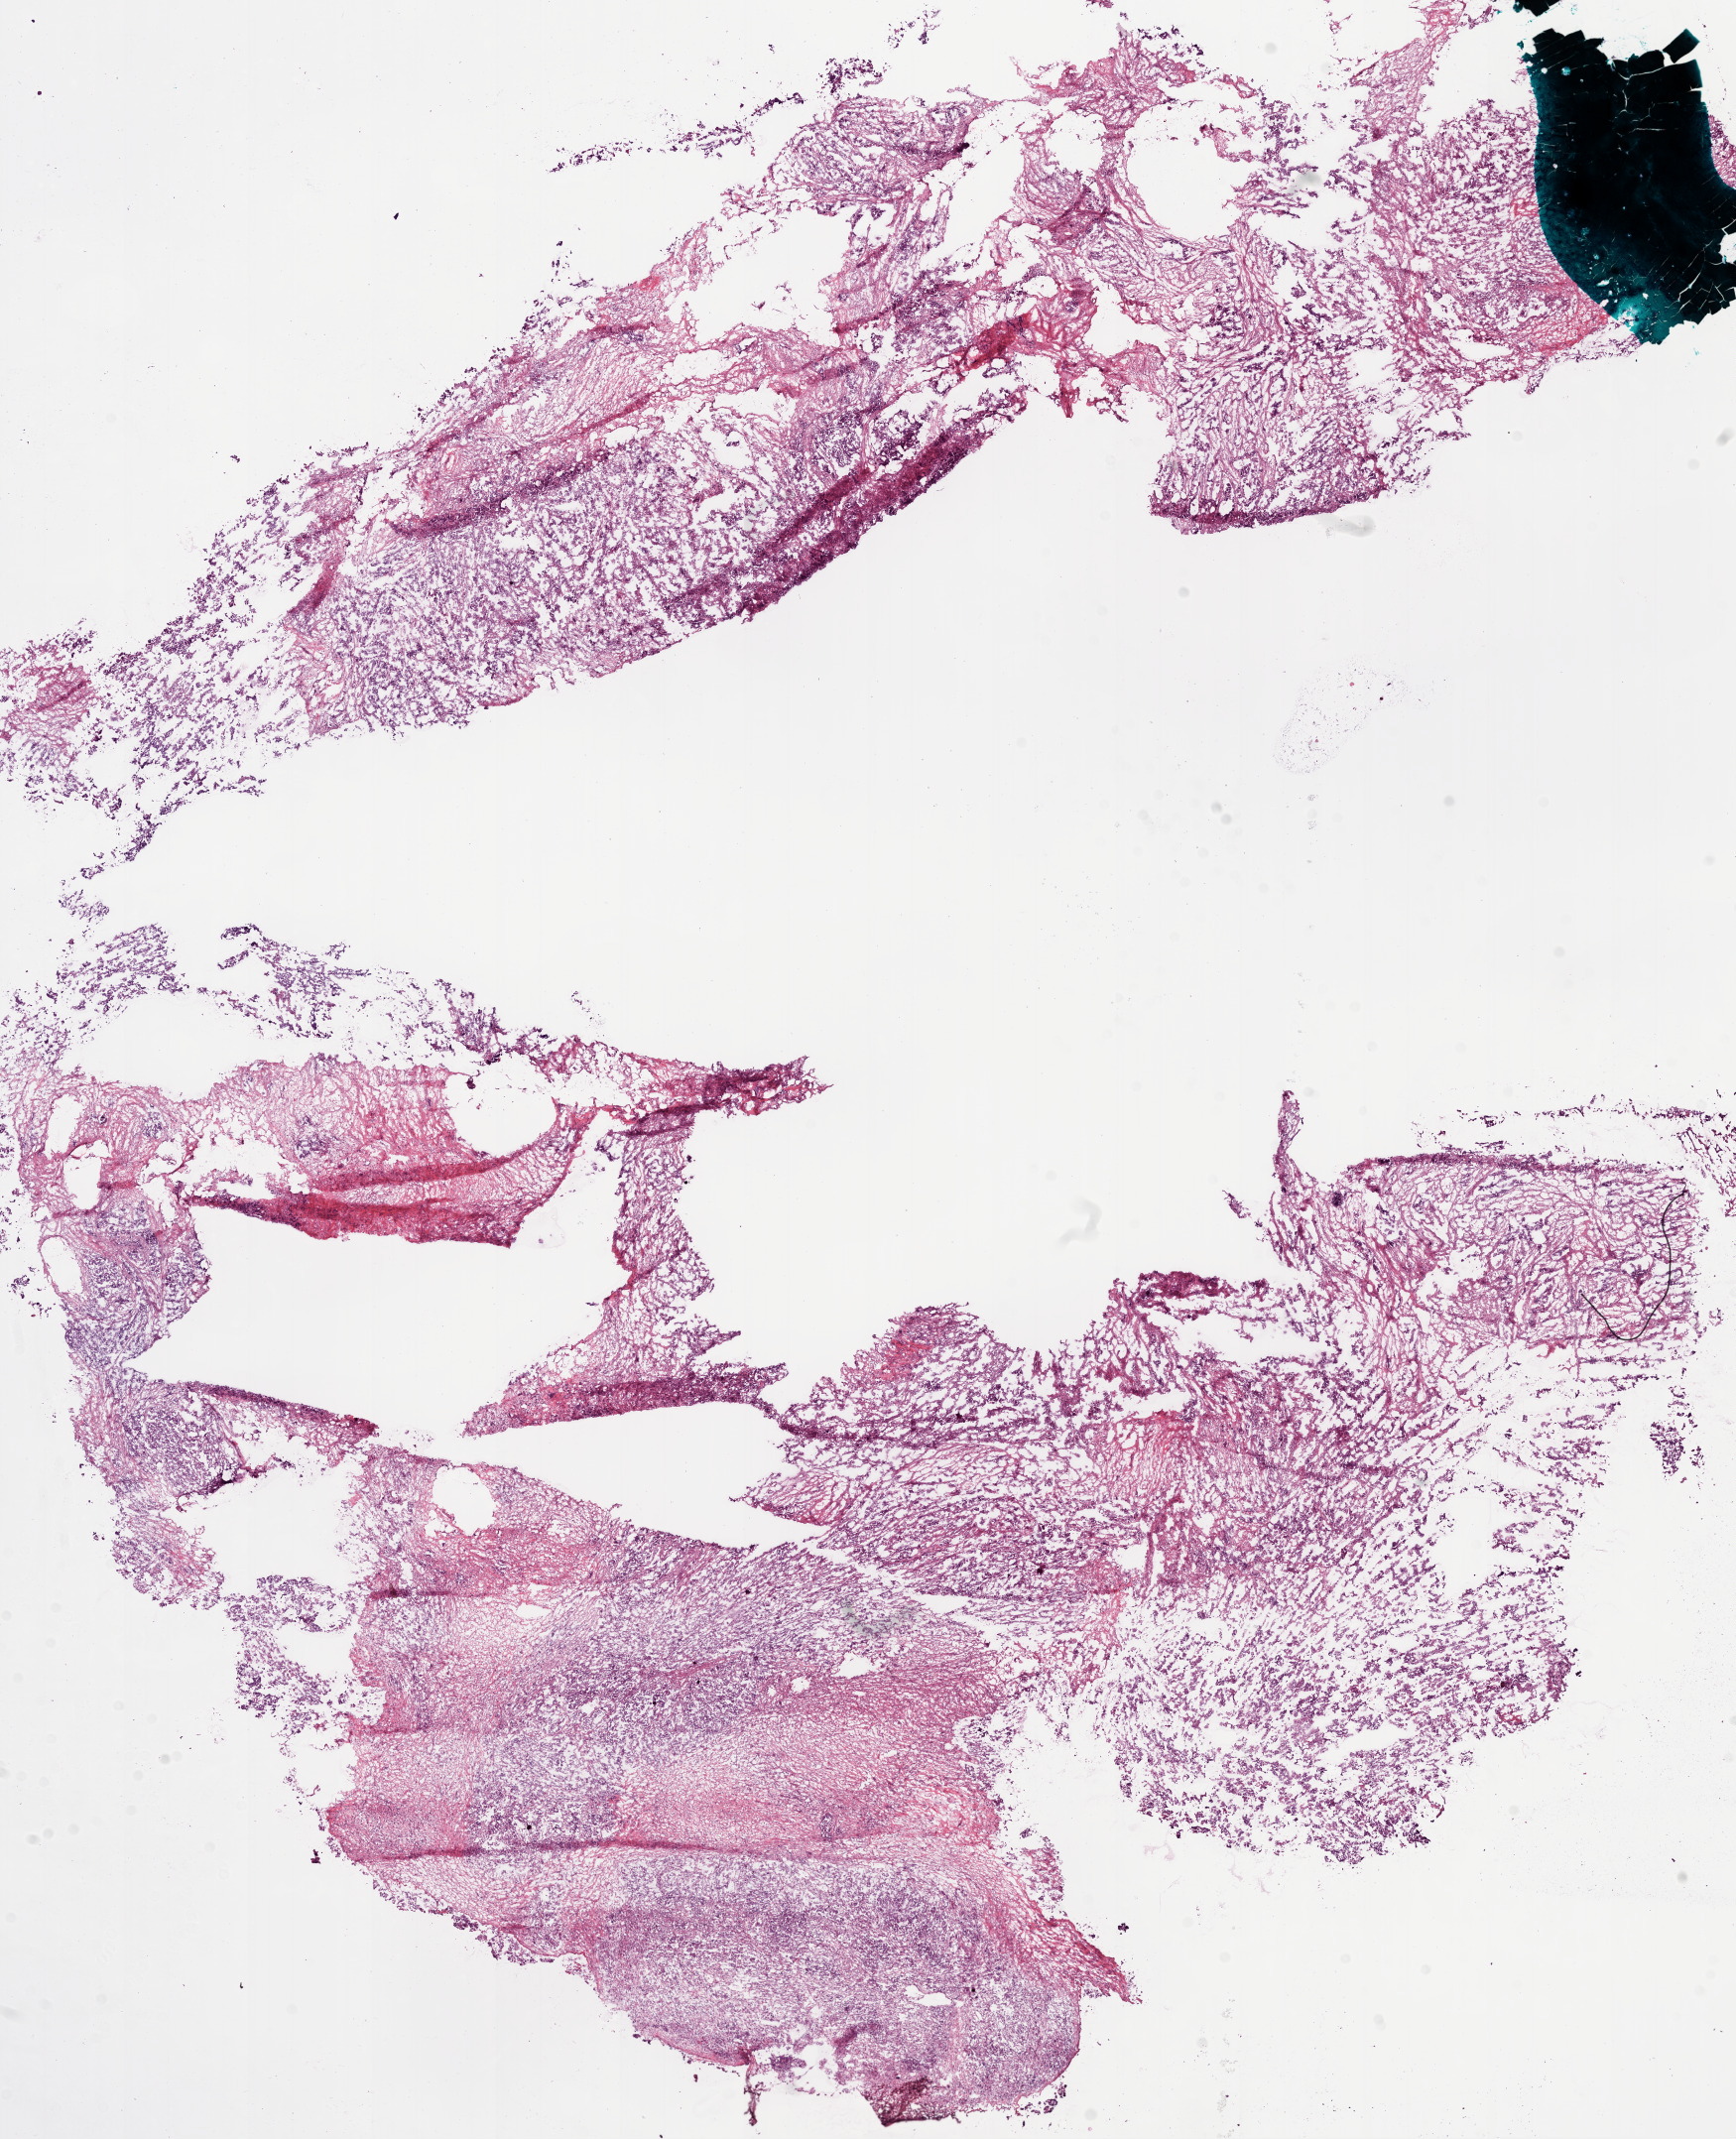
Digitized H&E tissue section (whole slide), a low-resolution overview of the entire scanned area, about 14.0 x 17.3 mm. Frozen section from the bottom of the tissue portion. Sample: primary tumour, ovary. Female patient; age at initial diagnosis 53 years. Histologic grade: G3 (poorly differentiated). Pathologist review of this section (percent, as recorded): tumour cells 79%, tumour nuclei 80%, normal cells 0%, stromal cells 20%, necrosis 1%.
FIGO stage: IIIC. Diagnosis: Serous cystadenocarcinoma, NOS.